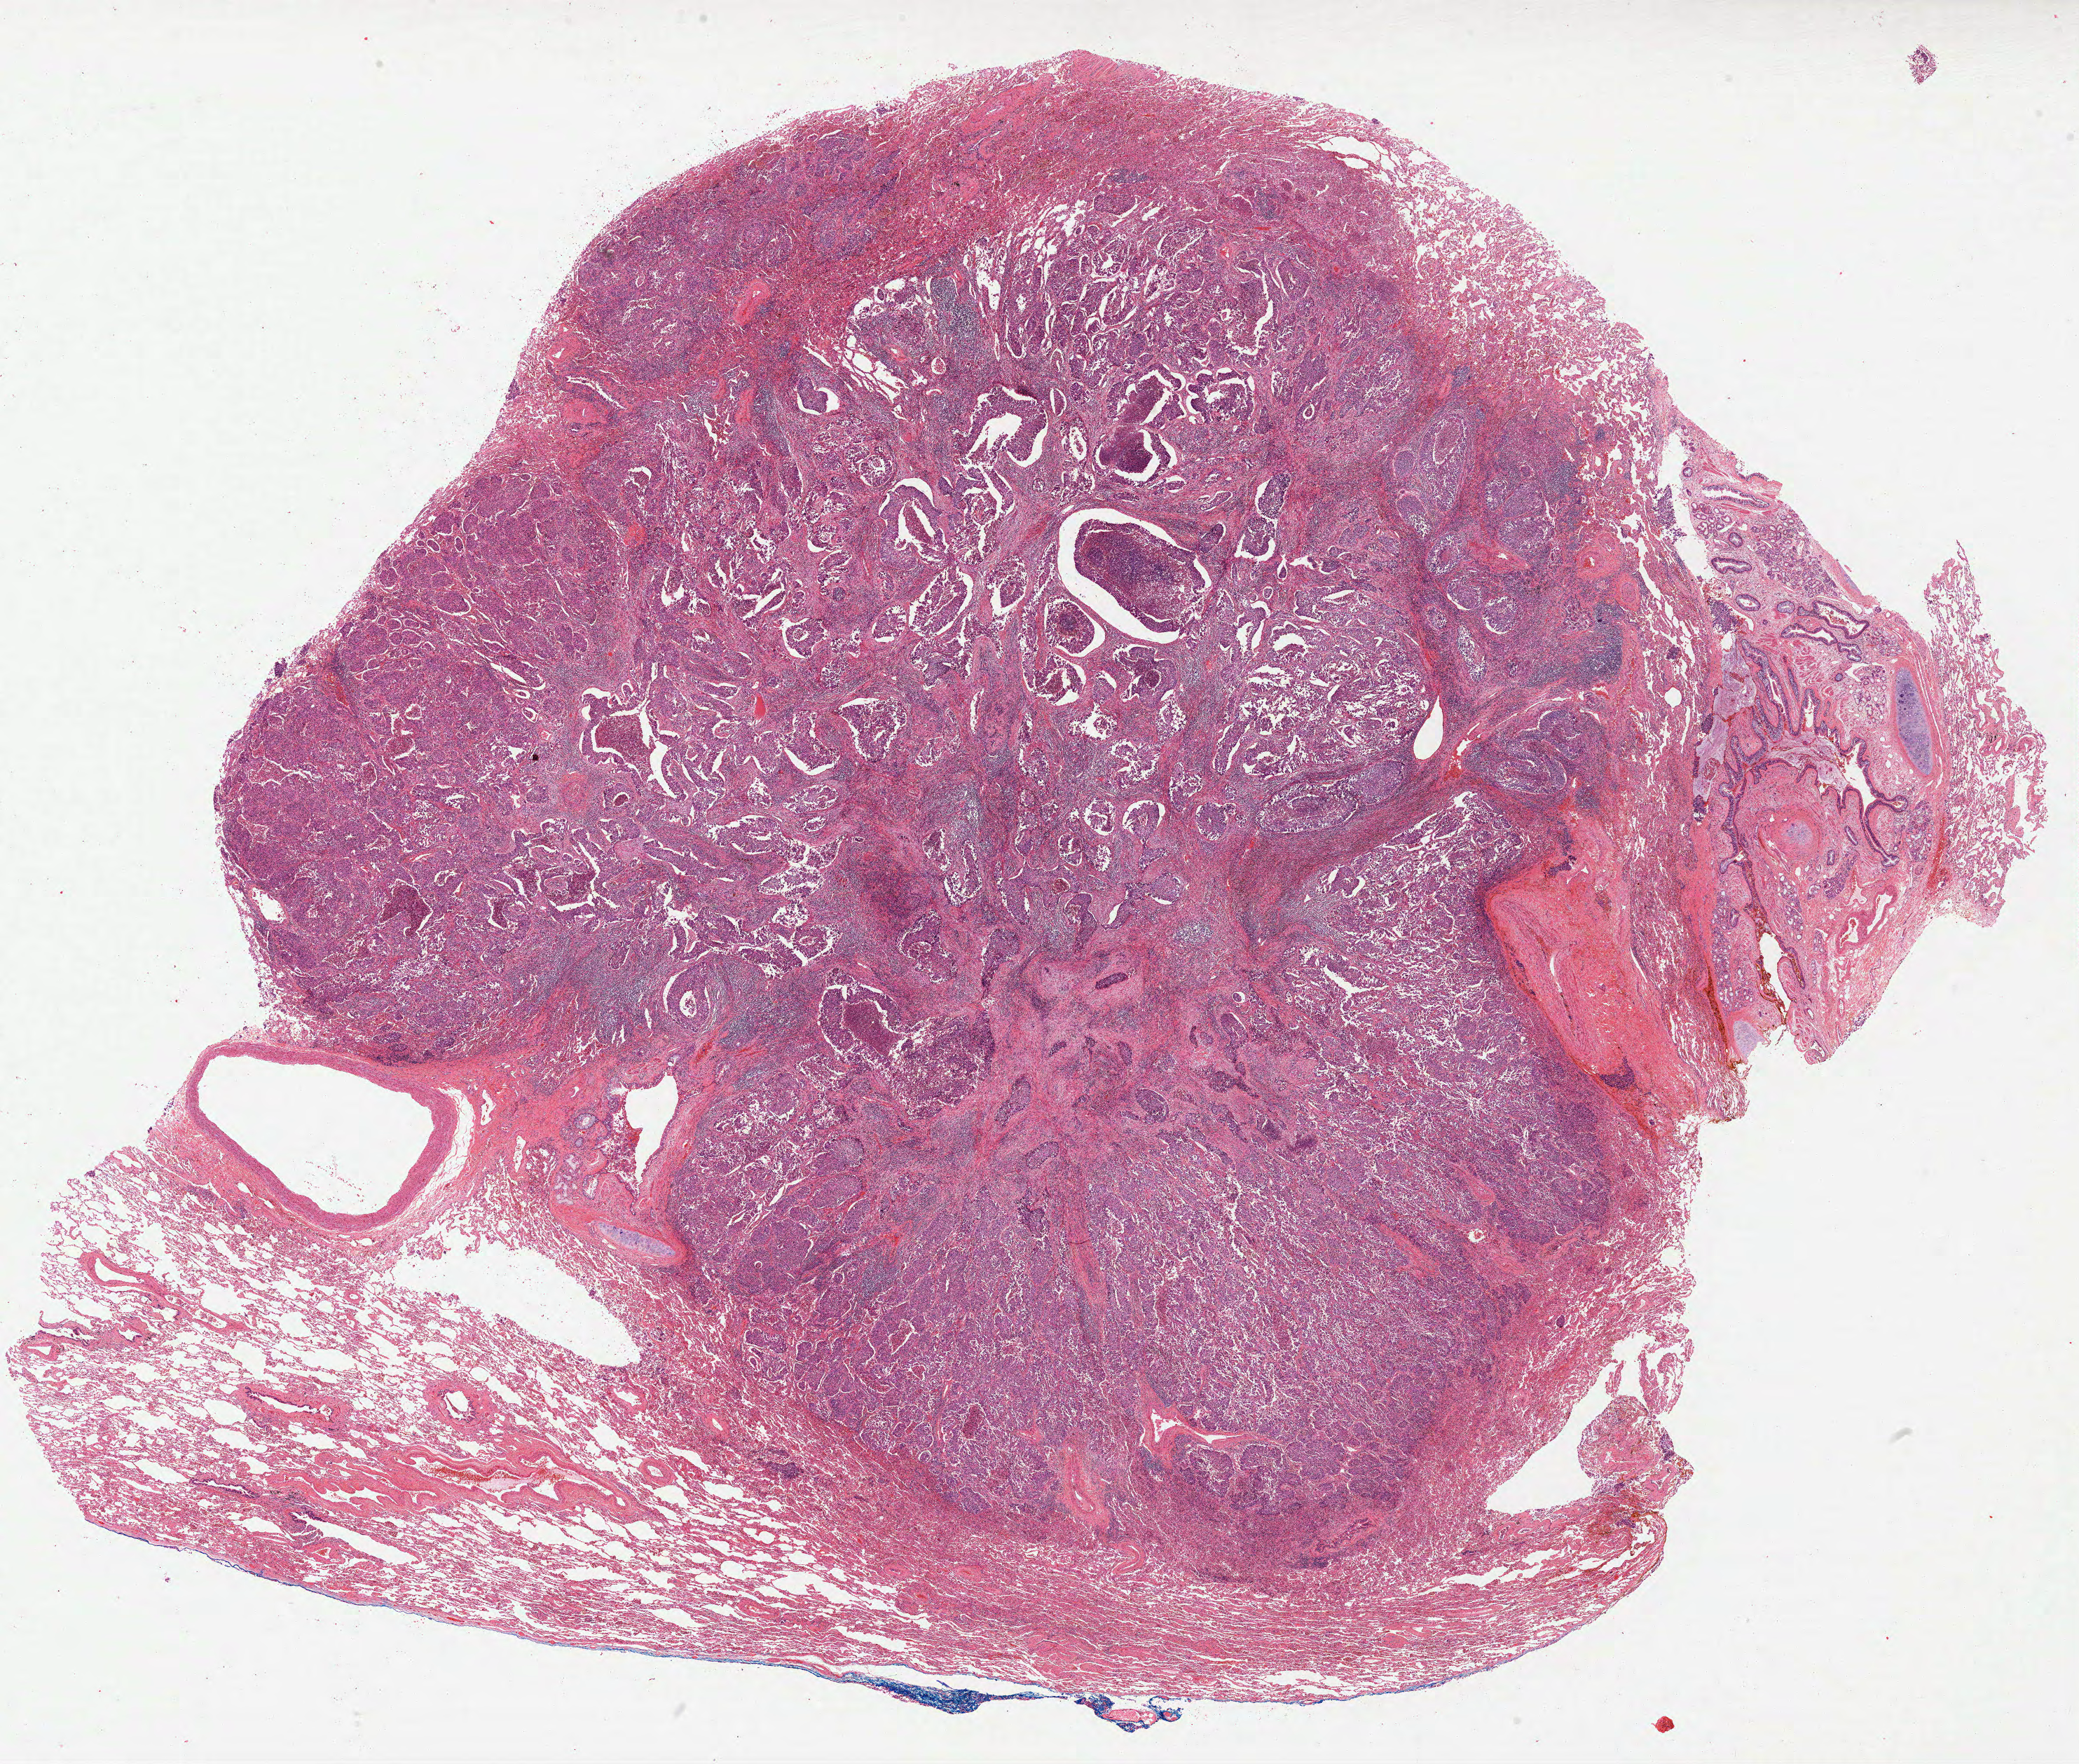
Digitized H&E tissue section (whole slide), a low-resolution overview of the entire scanned area, about 23.9 x 20.3 mm; FFPE section; primary tumour sample from the lung. Male, age 66 years at initial diagnosis.
AJCC pathologic stage: IA. TNM: T1a N0 MX. Laterality: right. Histologic diagnosis: Squamous cell carcinoma, NOS (upper lobe, lung).